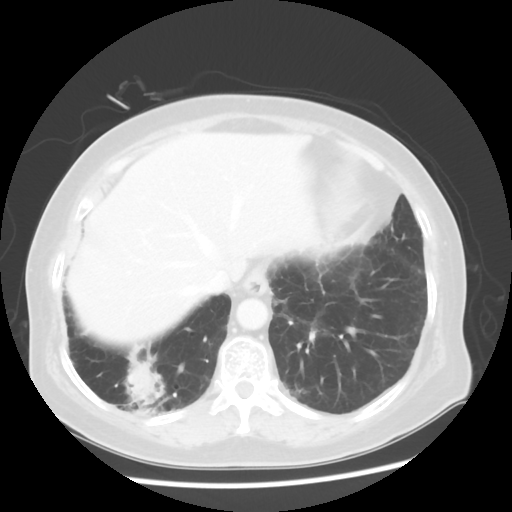
Chest CT, one axial slice; slice 14 of 56 in the series (ordered by position); reconstruction kernel STANDARD; 120 kVp; lung window (W 1500 / L -600 HU); 5 mm slice thickness; 512 × 512 image matrix. Female patient, age 64 years. Case-level facts recorded for this patient, not image findings: clinical TNM (as recorded): Tis N0 M0.
Outlined on this slice (bounding box drawn by a radiologist):
- lung tumour (recorded histology: adenocarcinoma): bounding box (x1, y1, x2, y2) in pixels: (119, 339, 174, 424)